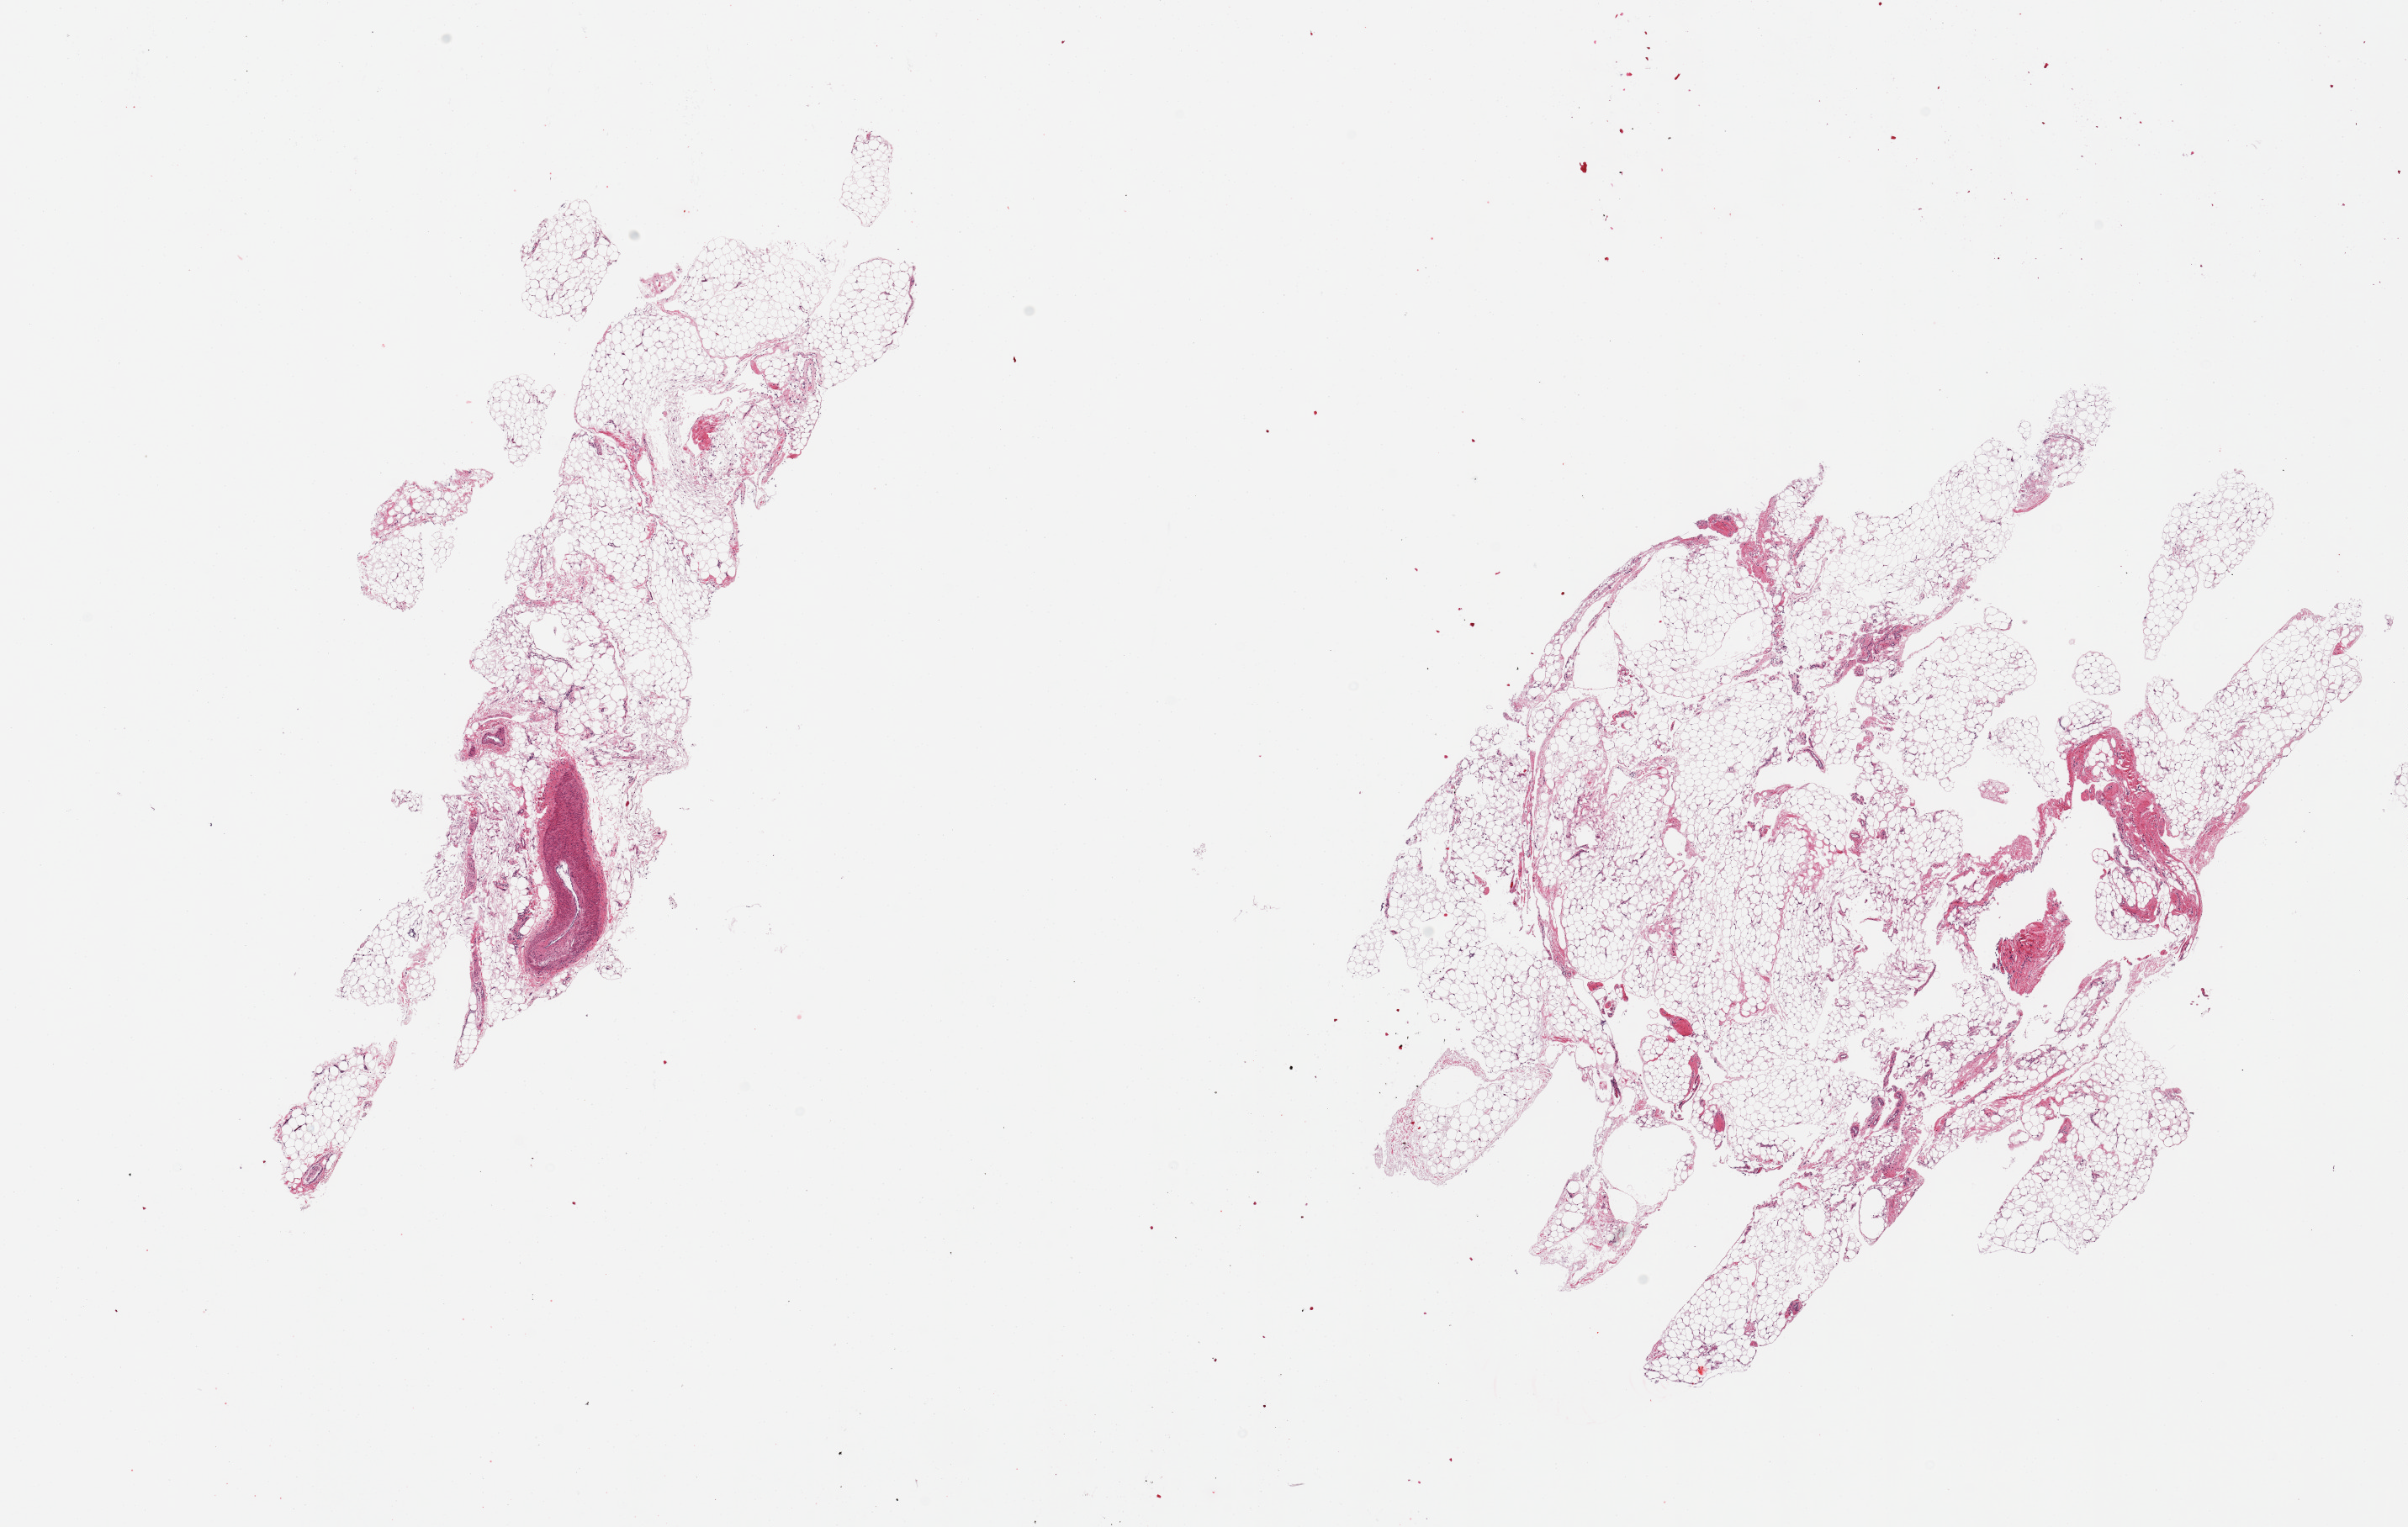
Digitized haematoxylin and eosin-stained section, brightfield — low-resolution overview of the scanned area, about 22.6 x 14.4 mm; PAXgene-fixed paraffin-embedded (PFPE) section; sampled site (target tissue): omentum; tissue donor sample. Male donor.
Review note (as recorded): 2 pieces; smaller piece includes large vessel/nerve.